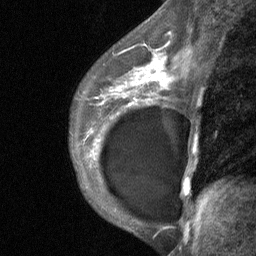
Breast MRI (dynamic contrast-enhanced), one sagittal slice; slice 44 of 64 in the series (ordered by position); dynamic contrast-enhanced study with each time point stored as its own series, time point 2 of 3 at this slice position (early post-contrast, ordered by acquisition time); 1.5 T; TE 4.8 ms, TR 27 ms; 2 mm slice thickness; 256 × 256 image matrix, field of view 180 × 180 mm. Patient: female, 35 years. Case-level facts recorded for this patient, not image findings: setting: breast cancer imaged before/during neoadjuvant chemotherapy; receptor status: HR-positive, HER2-negative.
Outlined on this slice (semi-automatically segmented with operator editing):
- analysis volume of interest (the breast-tissue region the enhancement analysis was run in; not a lesion): bounding box (x1, y1, x2, y2) in pixels: (74, 58, 180, 171)
- tumour enhancement mask (voxels above the 90 % enhancement threshold inside the analysis volume of interest): (137, 60, 168, 88)